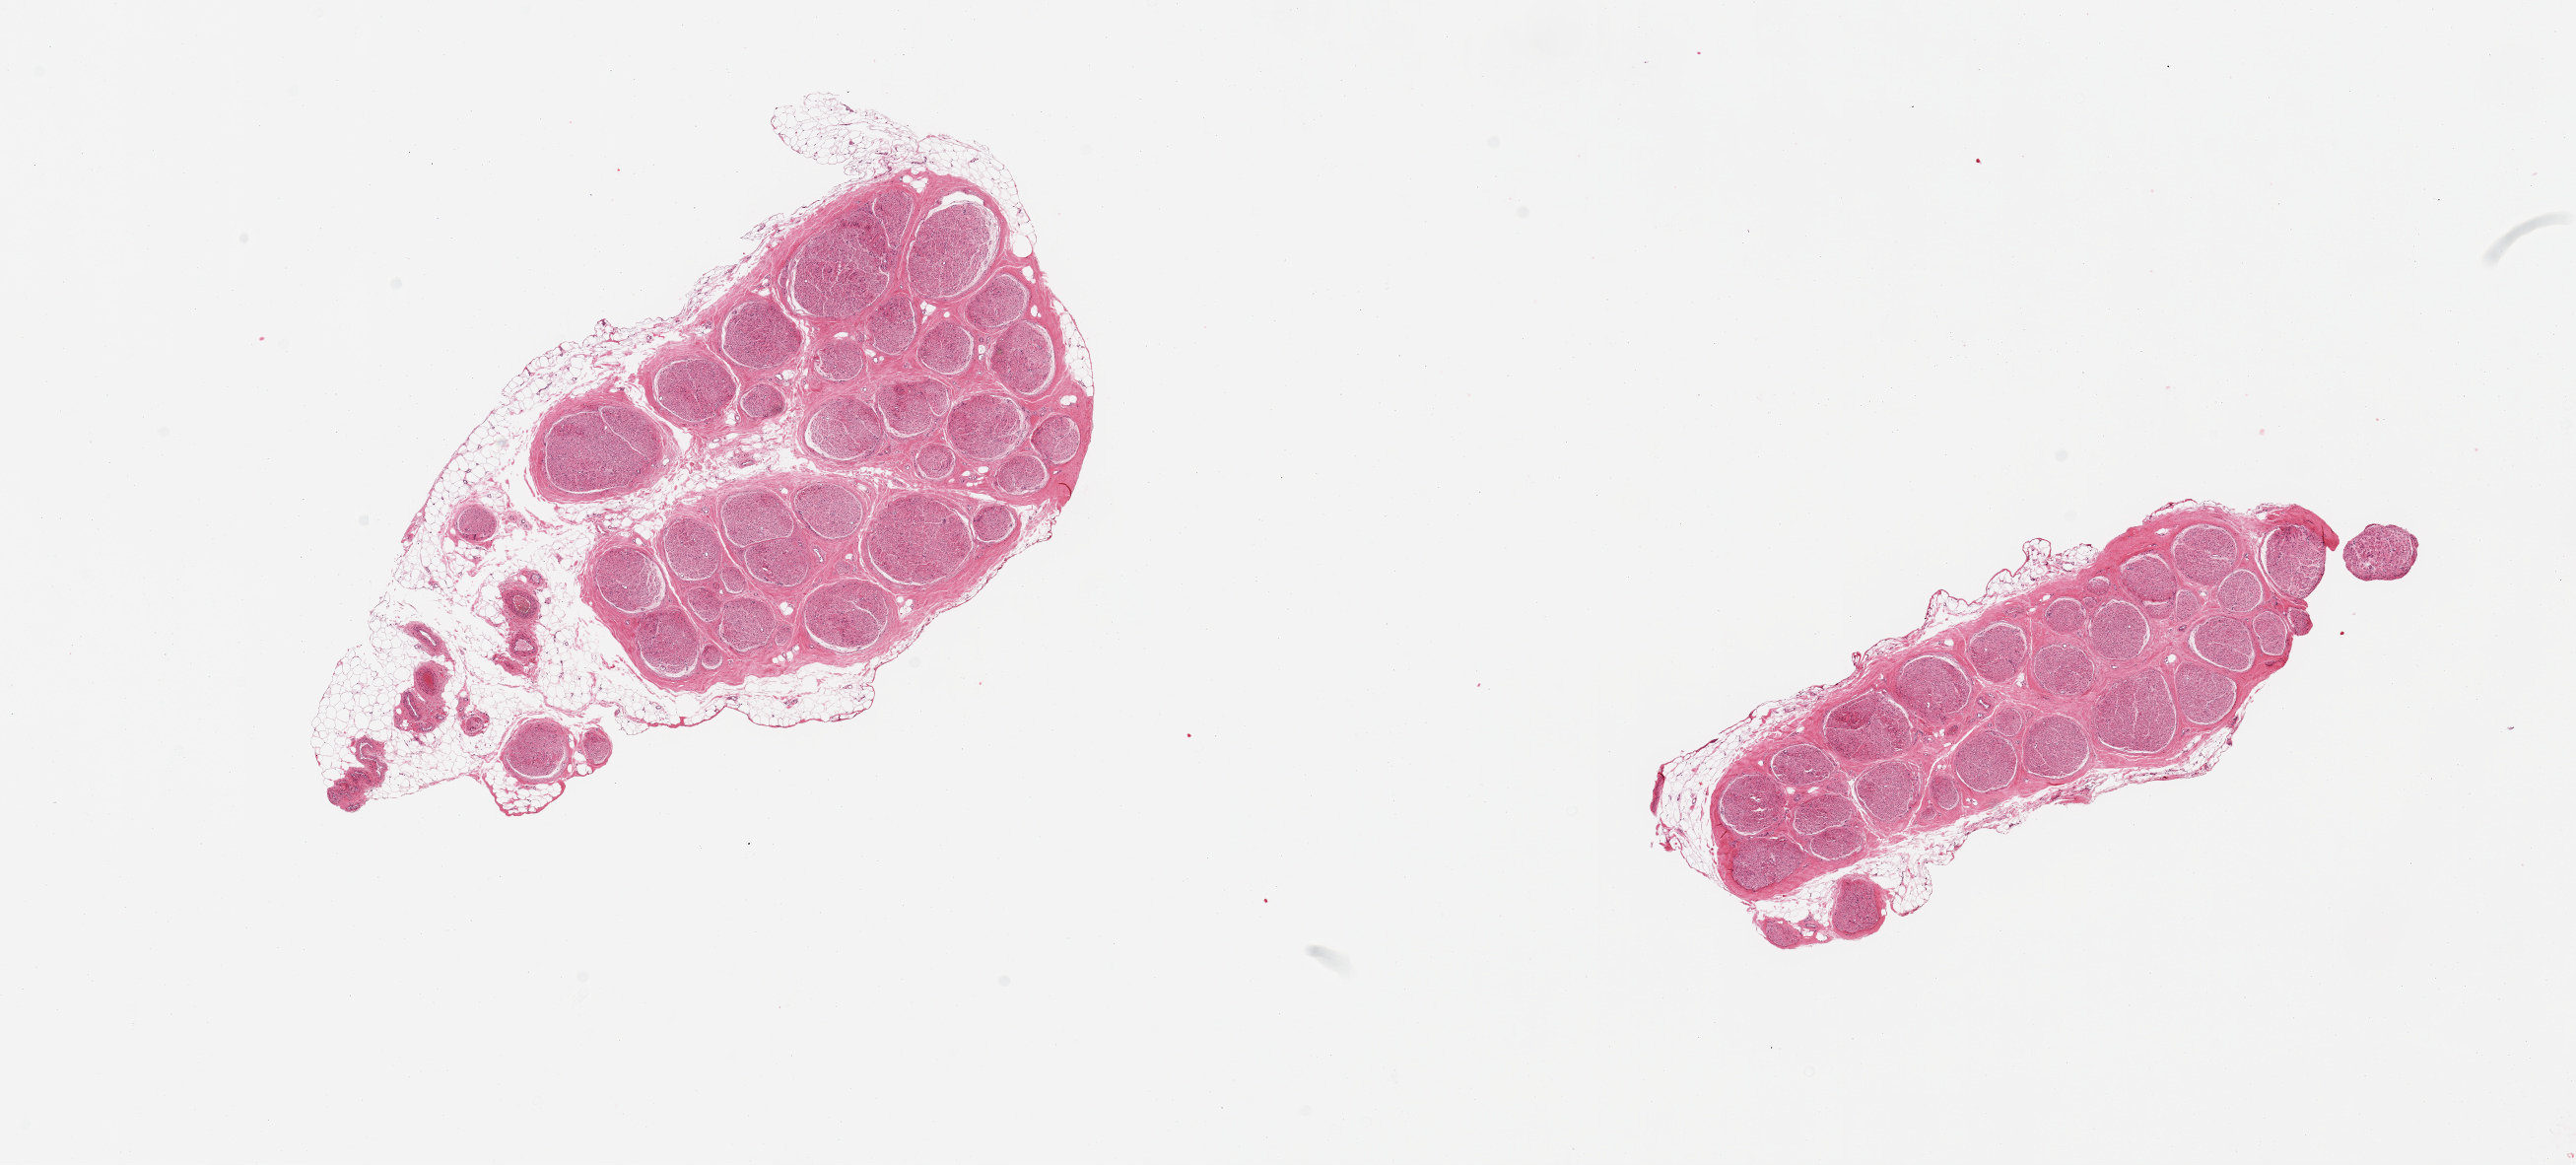
Digitized haematoxylin and eosin-stained section — whole scanned area (about 20.7 x 9.3 mm) shown as a low-resolution overview; PAXgene-fixed, paraffin-embedded tissue; target tissue: tibial nerve; tissue donor sample. Donor: female.
Reviewer comment on this tissue sample: 2 pieces; 10 & 20% internal and external fat.